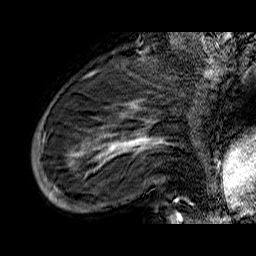
Breast MRI (dynamic contrast-enhanced), one sagittal slice. Position 15 of 60 along the scan axis. Dynamic contrast-enhanced series, time point 2 of 6 at this slice position (early post-contrast). 1.5 T. TE 6.5 ms, TR 32.9 ms. 4 mm slice thickness. 256 × 256 image matrix. Female patient. From the clinical record (not read from this slice): setting: breast cancer imaged before/during neoadjuvant chemotherapy; receptor status: HR-positive, HER2-negative.
Structures marked on this image (semi-automatically segmented with operator editing):
- analysis volume of interest (the breast-tissue region the enhancement analysis was run in; not a lesion): bounding box <33,74,176,210> (left, top, right, bottom; pixels)
- tumour enhancement mask (voxels above the 100 % enhancement threshold inside the analysis volume of interest): <37,74,176,203>